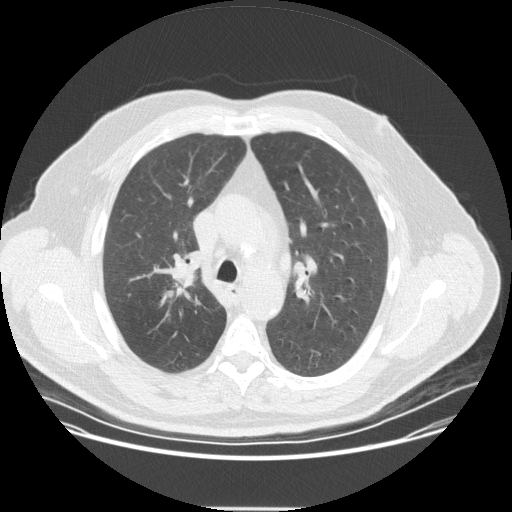
Chest CT (low-dose screening protocol), one axial image, second screening round (one year after baseline), lung window (W 1500 / L -600 HU), slice 116 of 351 in the series, 512 × 512 image matrix, field of view 419 × 419 mm. Male participant, aged 57 years at enrolment. Current smoker at enrolment.
Lesion marked by an expert reader, bounding box (x1, y1, x2, y2) in pixels: (146, 249, 211, 312). Screening reader's record for this exam (one nodule recorded; not confirmed to be the boxed lesion): non-calcified nodule or mass ≥4 mm, right upper lobe, 20 × 16 mm, spiculated (stellate) margins, soft tissue attenuation, pre-existing on the prior screen: no. Official screen result: positive, other. Participant outcome: lung cancer diagnosed 35 days after this screen — non-small cell carcinoma, right upper lobe, poorly differentiated (G3), stage IIA (AJCC 6th edition), 25 mm at pathology.